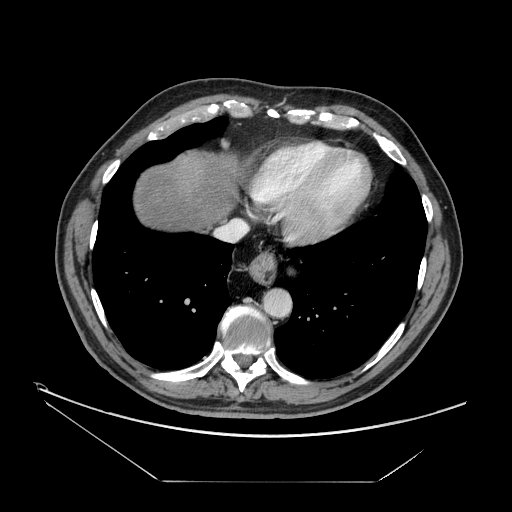
Contrast-enhanced abdominal CT, one axial slice. Slice 149 of 161 in the series (ordered by position). Reconstruction kernel STANDARD. Soft-tissue window (W 400 / L 40 HU). 2.5 mm slice thickness. 512 × 512 image matrix, field of view 440 × 440 mm. Male patient, age 65 years. From the clinical record (not read from this slice): diagnosis: colorectal cancer liver metastases, imaged before liver resection; multiple liver metastases: yes; largest metastasis: 4.2 cm.
Outlined on this slice (expert manual segmentation):
- hepatic veins: box from (x=216, y=177) to (x=267, y=241) px
- liver: (x=134, y=151)–(x=236, y=231)
- planned liver remnant (the part of the liver to remain after resection): (x=133, y=151)–(x=236, y=231)